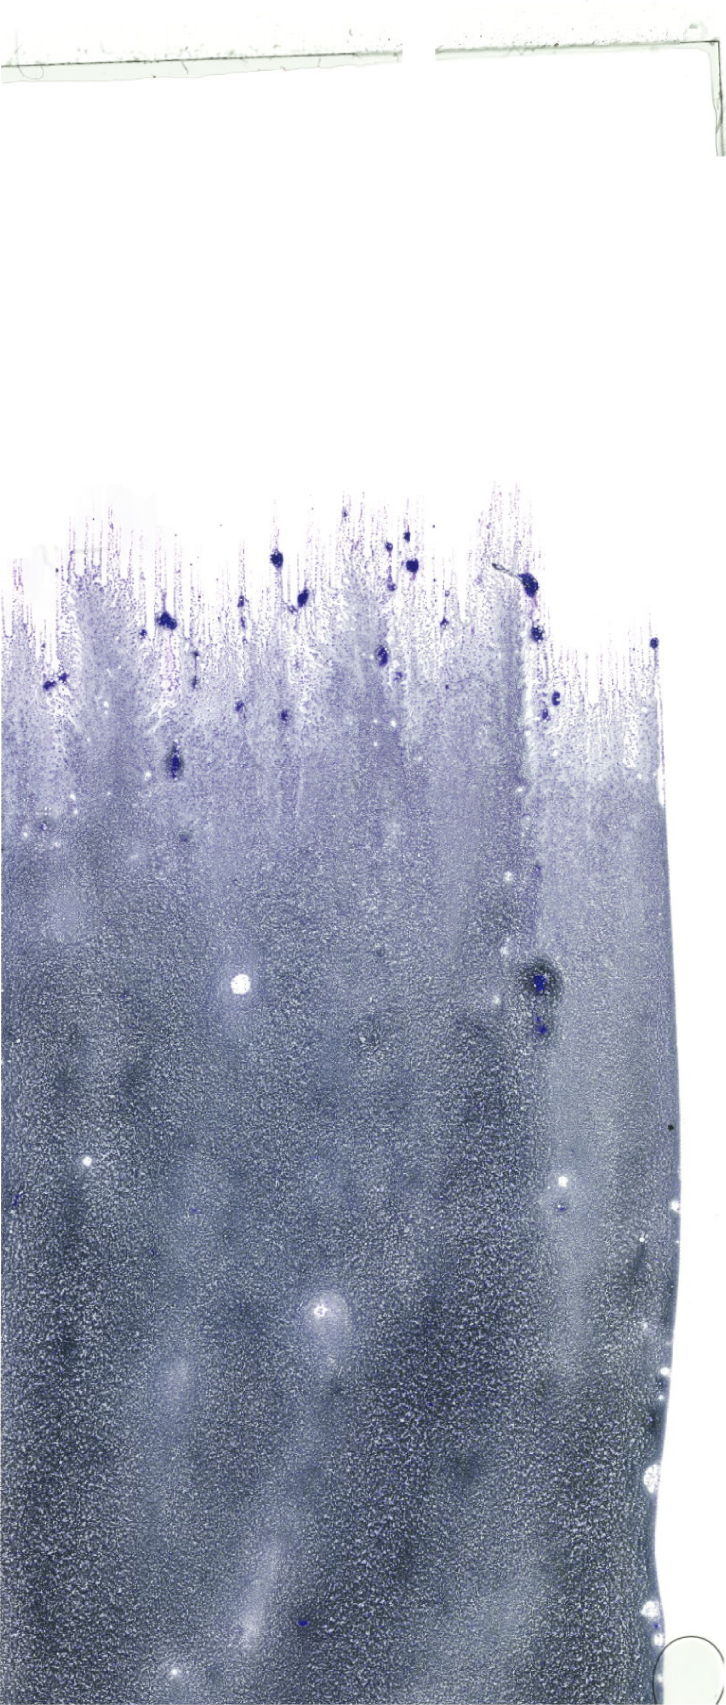
May-Grünwald-Giemsa (MGG)-stained marrow aspirate smear (whole slide) — low-resolution overview of the scanned area, about 20.6 x 48.3 mm. Male patient.
• diagnosis: Acute Myeloid Leukemia without Maturation